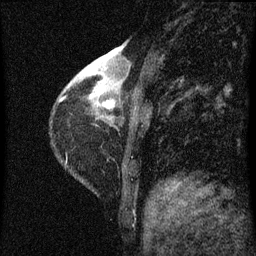
Breast MRI (dynamic contrast-enhanced), one sagittal slice; position 15 of 60 along the scan axis; dynamic contrast-enhanced series, image 2 of 3 at this slice position (ordered by acquisition); 1.5 T; TE 4.2 ms, TR 8 ms; 256 × 256 image matrix, field of view 180 × 180 mm. Female patient, age 38 years.
Annotated regions visible in this slice (semi-automatic segmentation, software-assisted and operator-edited):
- analysis volume of interest (the breast-tissue region the enhancement analysis was run in; not a lesion): bounding box [x1, y1, x2, y2] px = [67, 44, 144, 129]
- tumour enhancement mask (voxels above the 70 % enhancement threshold inside the analysis volume of interest): [89, 58, 114, 109]